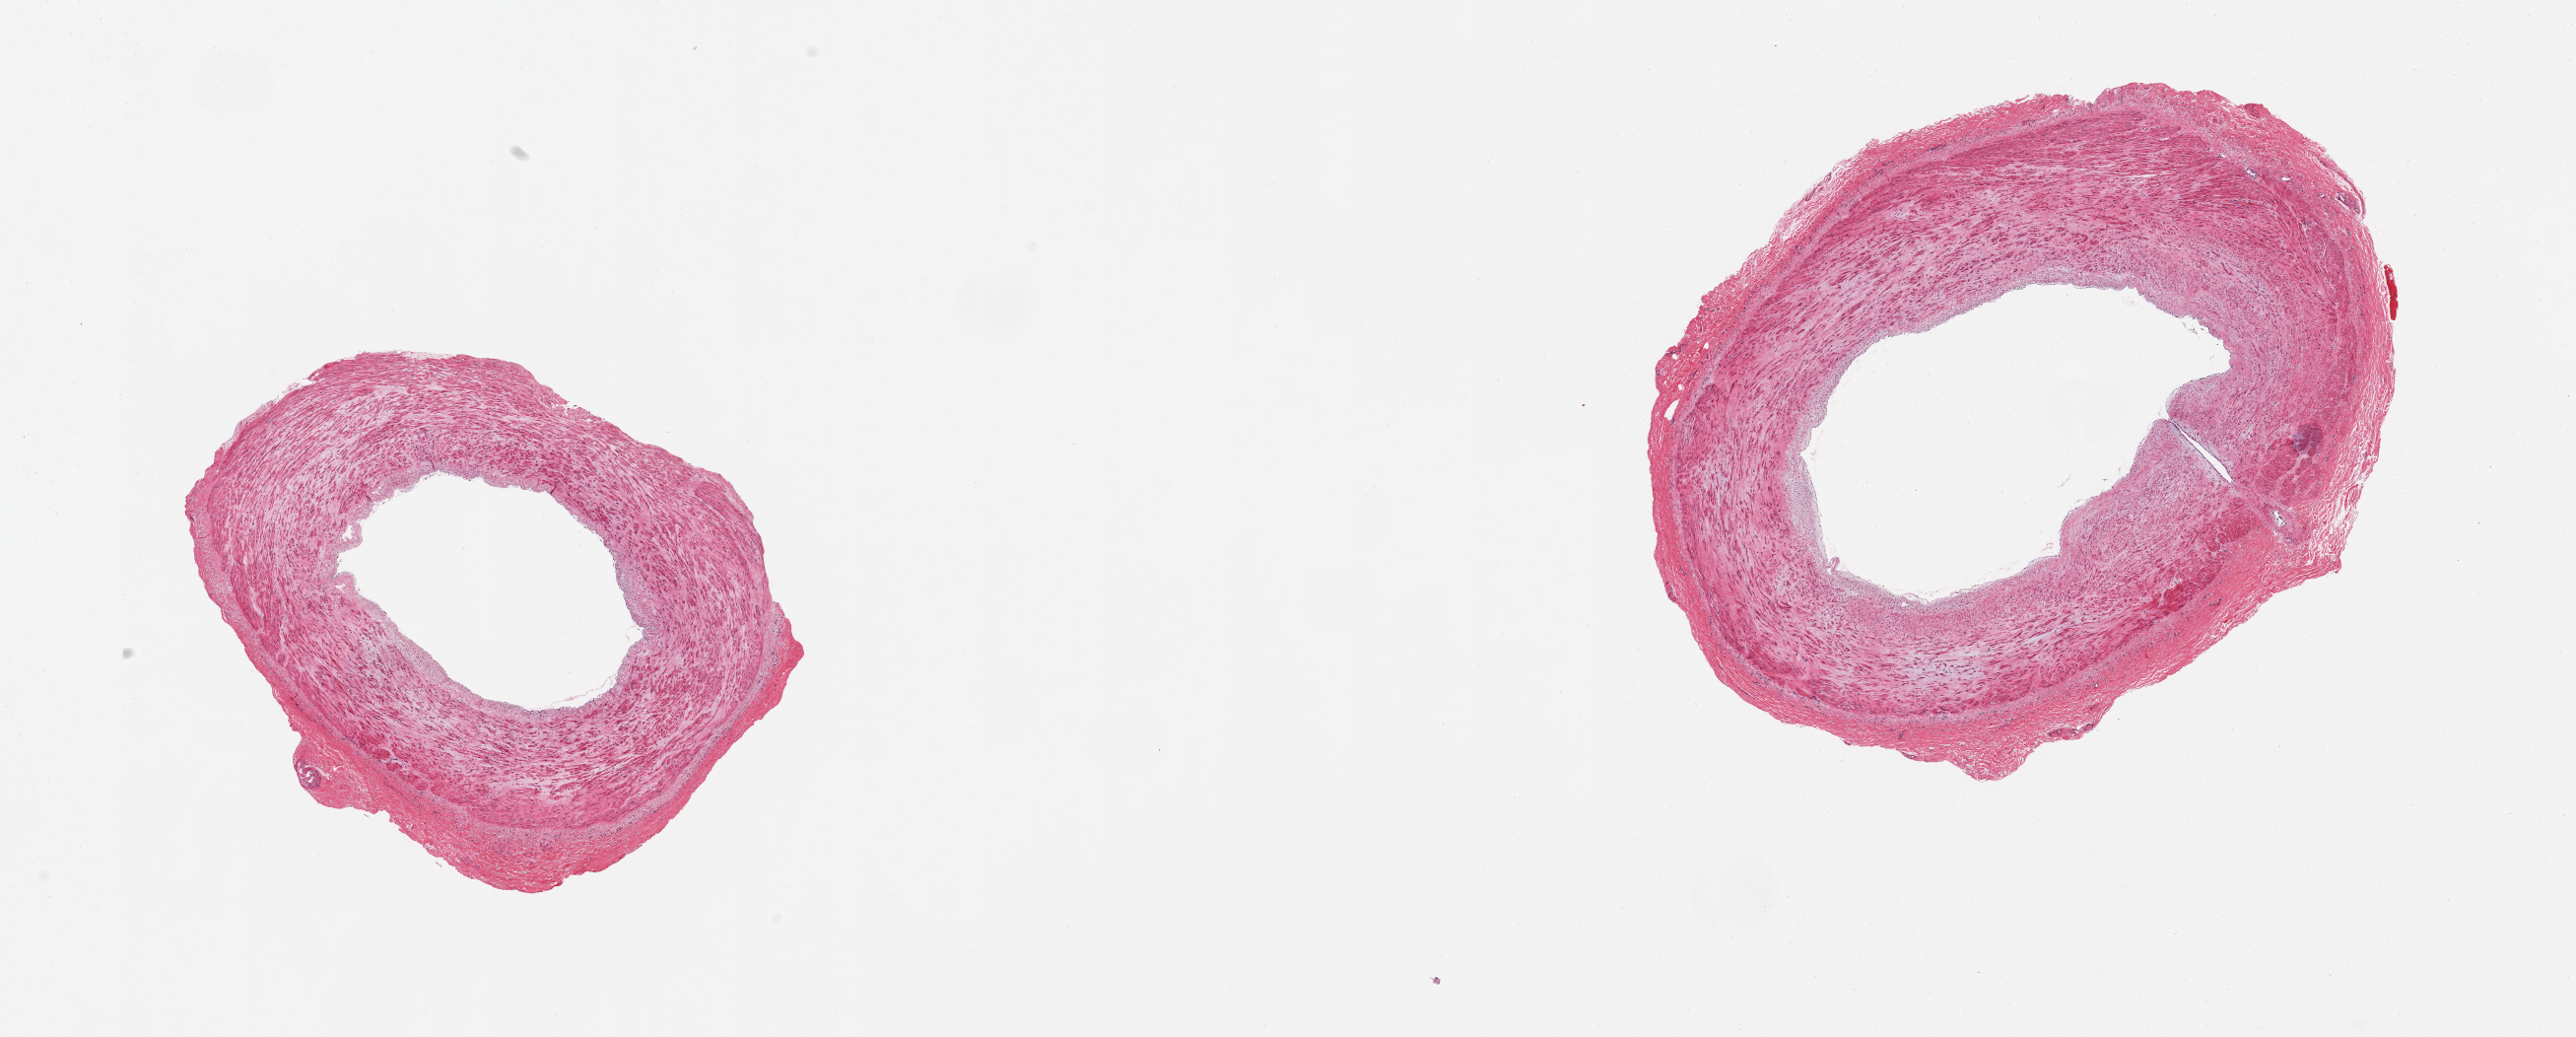
Haematoxylin and eosin whole-slide image, brightfield, low-resolution overview of the scanned area, about 20.7 x 8.3 mm (acquisition: 20x scan); PAXgene-fixed paraffin-embedded (PFPE) section; target tissue: tibial artery; donor tissue sample. Donor sex: female.
* review note (as recorded): 2 pieces; atherosis